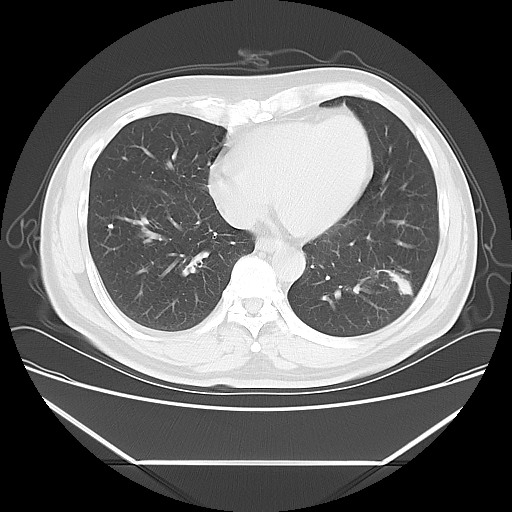
Chest CT, one axial slice; slice 21 of 57 in the series (ordered by position); reconstruction kernel LUNG; 120 kVp; lung window (W 1500 / L -600 HU); 5 mm slice thickness; 512 × 512 image matrix, field of view 384 × 384 mm. Patient: male, 53 years. From the clinical record (not read from this slice): clinical TNM (as recorded): T1c N0 M0.
Structures marked on this image (bounding box drawn by a radiologist):
- lung tumour (recorded histology: adenocarcinoma): bounding box <377,262,423,309> (left, top, right, bottom; pixels)